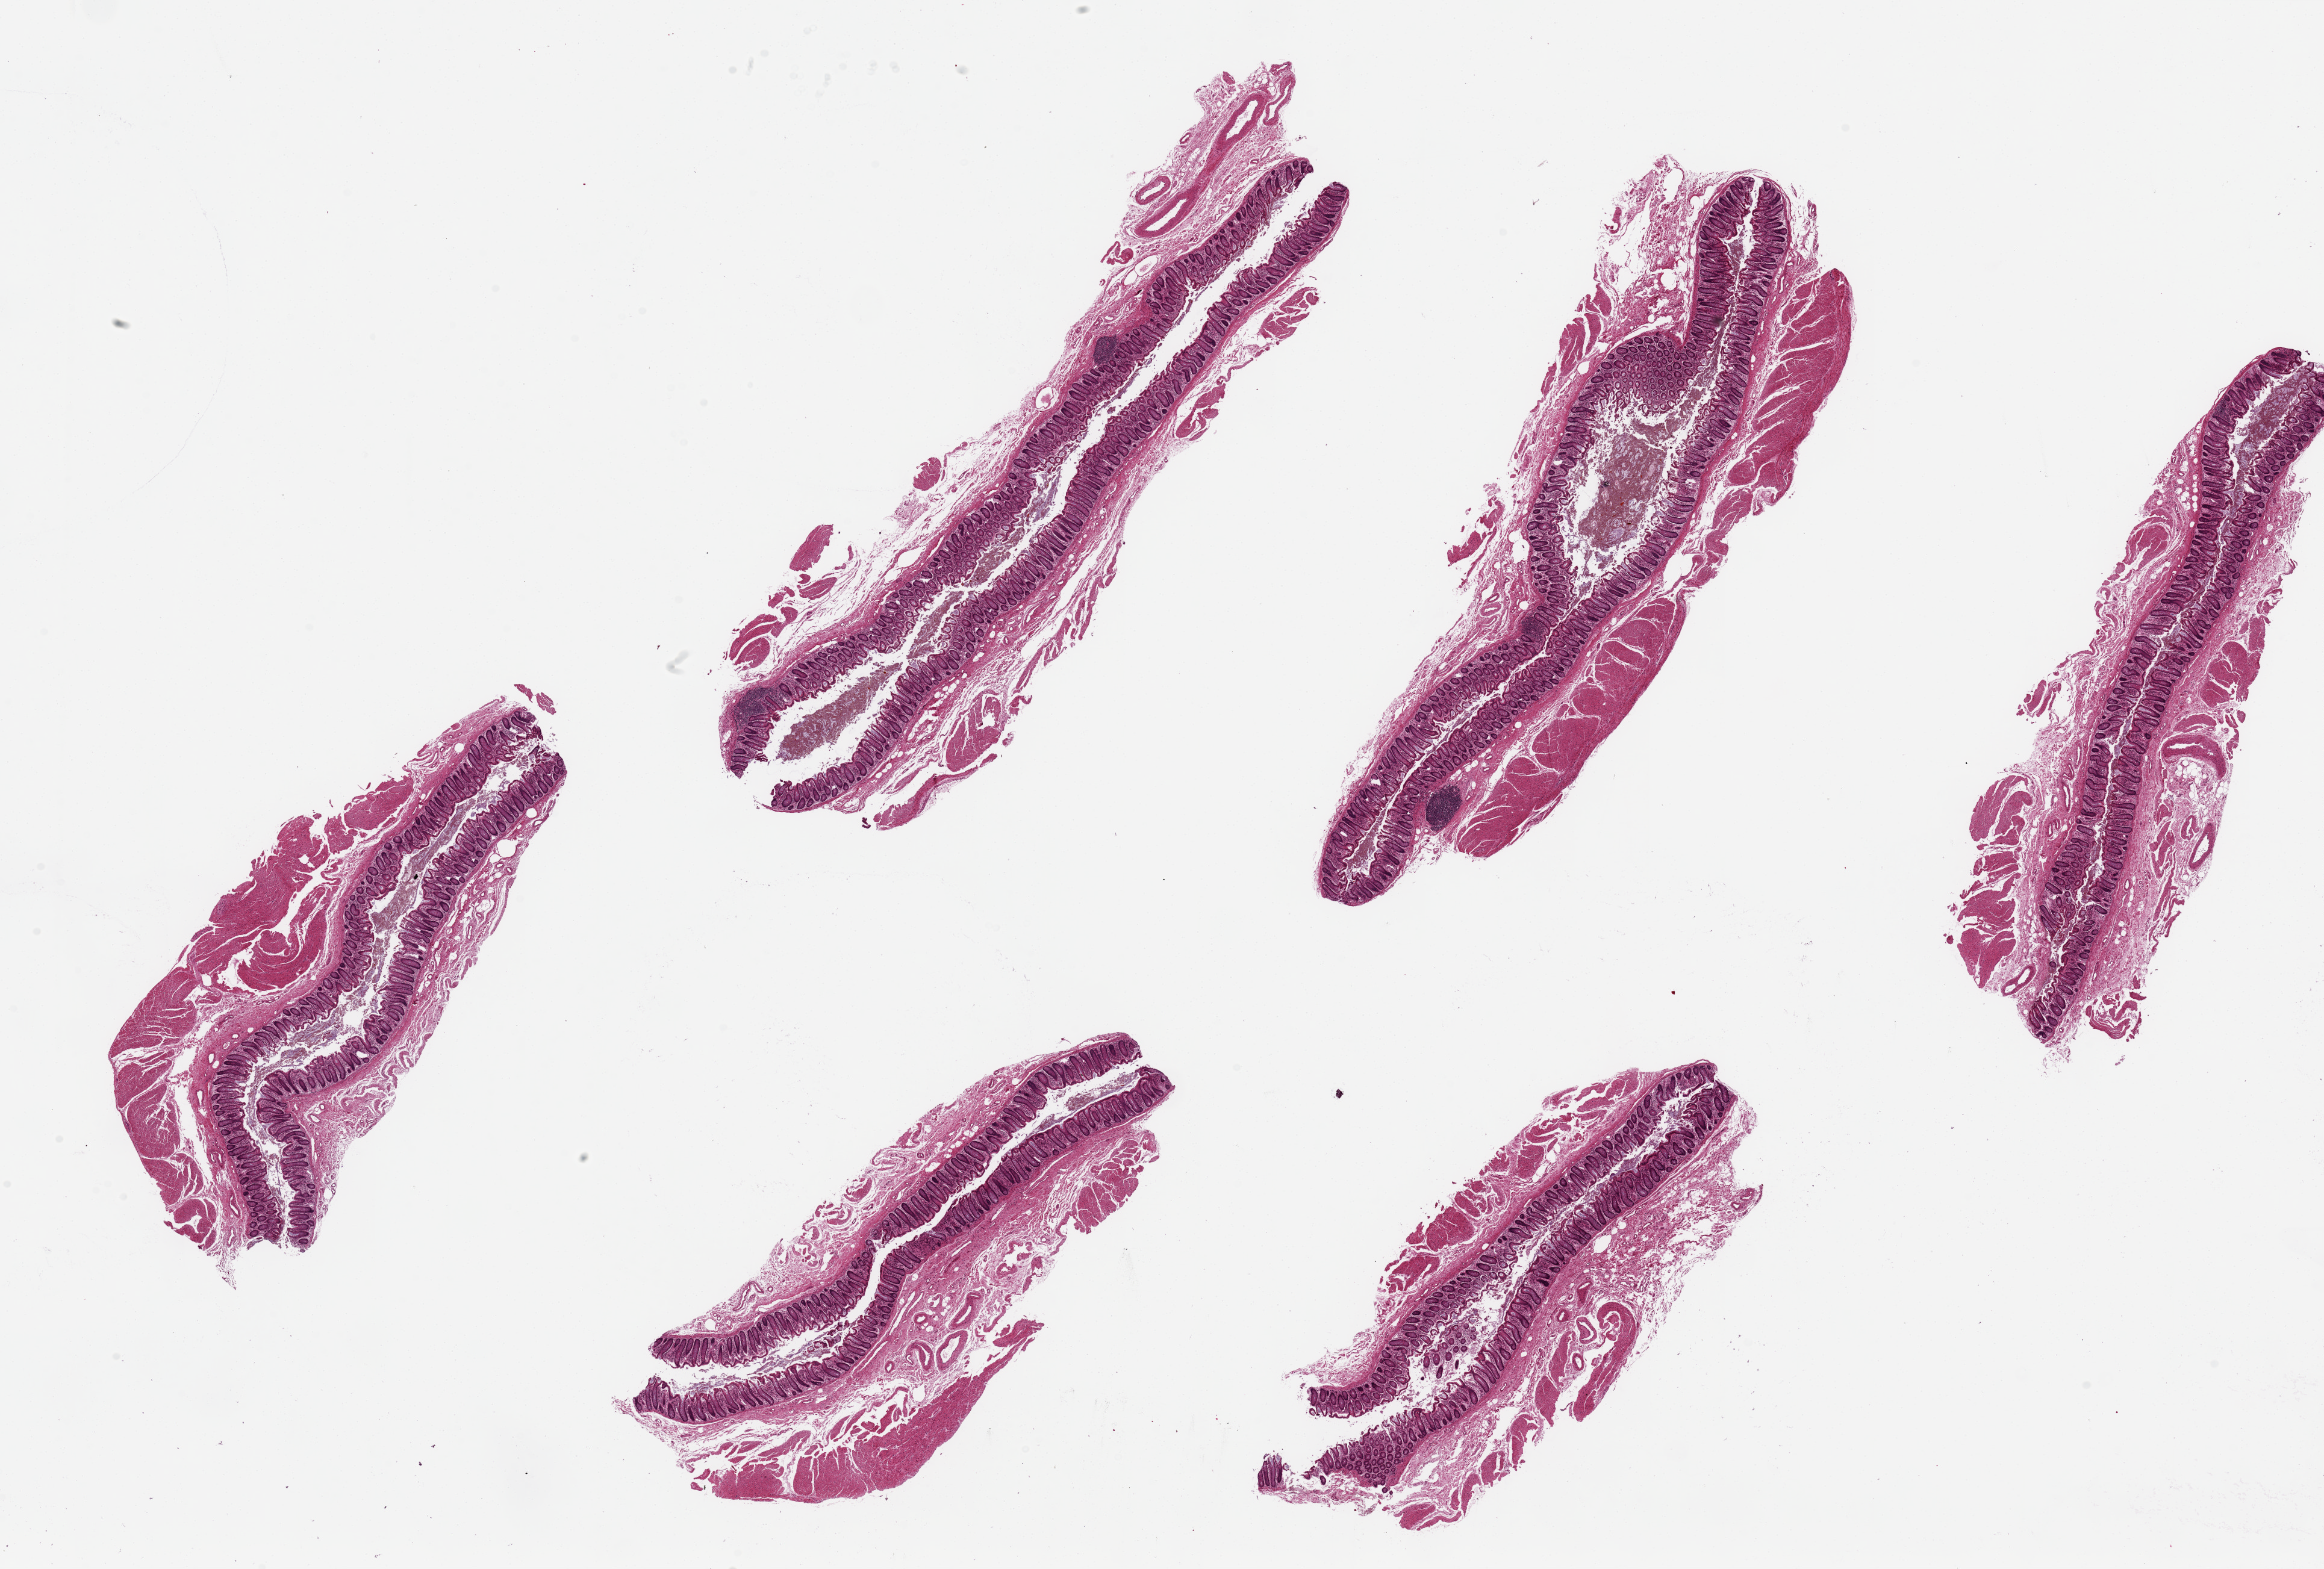
Haematoxylin and eosin whole-slide image, brightfield, shown as a low-resolution overview of the whole scanned area (about 30.5 x 20.6 mm, slide scanned at 20x); PAXgene-fixed paraffin-embedded (PFPE) section; section of transverse colon (target tissue); tissue donor sample. Donor sex: male.
Pathologist's review note for this sample: 6 pieces up to 11x4 mm.